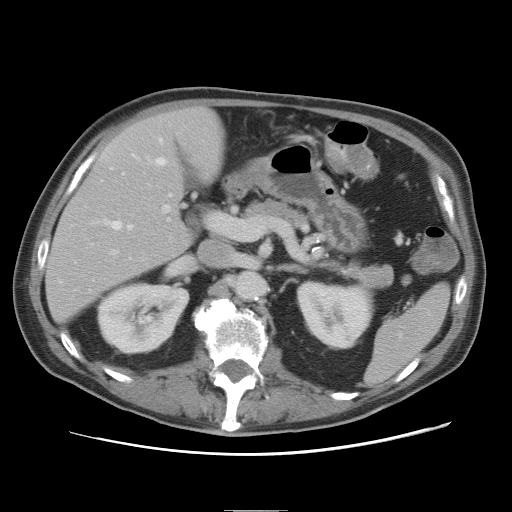
Contrast-enhanced abdominal CT, one axial slice. Slice 39 of 89 in the series (ordered by position). 120 kVp. Intravenous contrast given. Soft-tissue window (W 400 / L 40 HU). 5 mm slice thickness. 512 × 512 image matrix, field of view 375 × 375 mm. Male patient, age 69 years. Case-level facts recorded for this patient, not image findings: diagnosis: colorectal cancer liver metastases, imaged before liver resection; multiple liver metastases: no; largest metastasis: 8.5 cm; disease in both lobes: no.
Outlined on this slice (manually delineated by an expert):
- hepatic veins: bounding box (x1, y1, x2, y2) in pixels: (105, 138, 171, 229)
- liver: (46, 108, 224, 321)
- planned liver remnant (the part of the liver to remain after resection): (46, 108, 224, 321)
- portal vein (with intrahepatic branches): (112, 205, 224, 254)